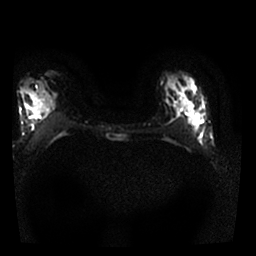
Breast MRI, one axial slice; position 14 of 25 along the scan axis; diffusion-weighted series; image 2 of 4 stored at this slice position (different b-values; order by instance number); 1.5 T; 4 mm slice thickness; 256 × 256 image matrix. Female patient.
Outlined on this slice (outlined manually by an expert reader):
- tumour on diffusion-weighted imaging: bounding box (x1, y1, x2, y2) in pixels: (175, 105, 206, 148)